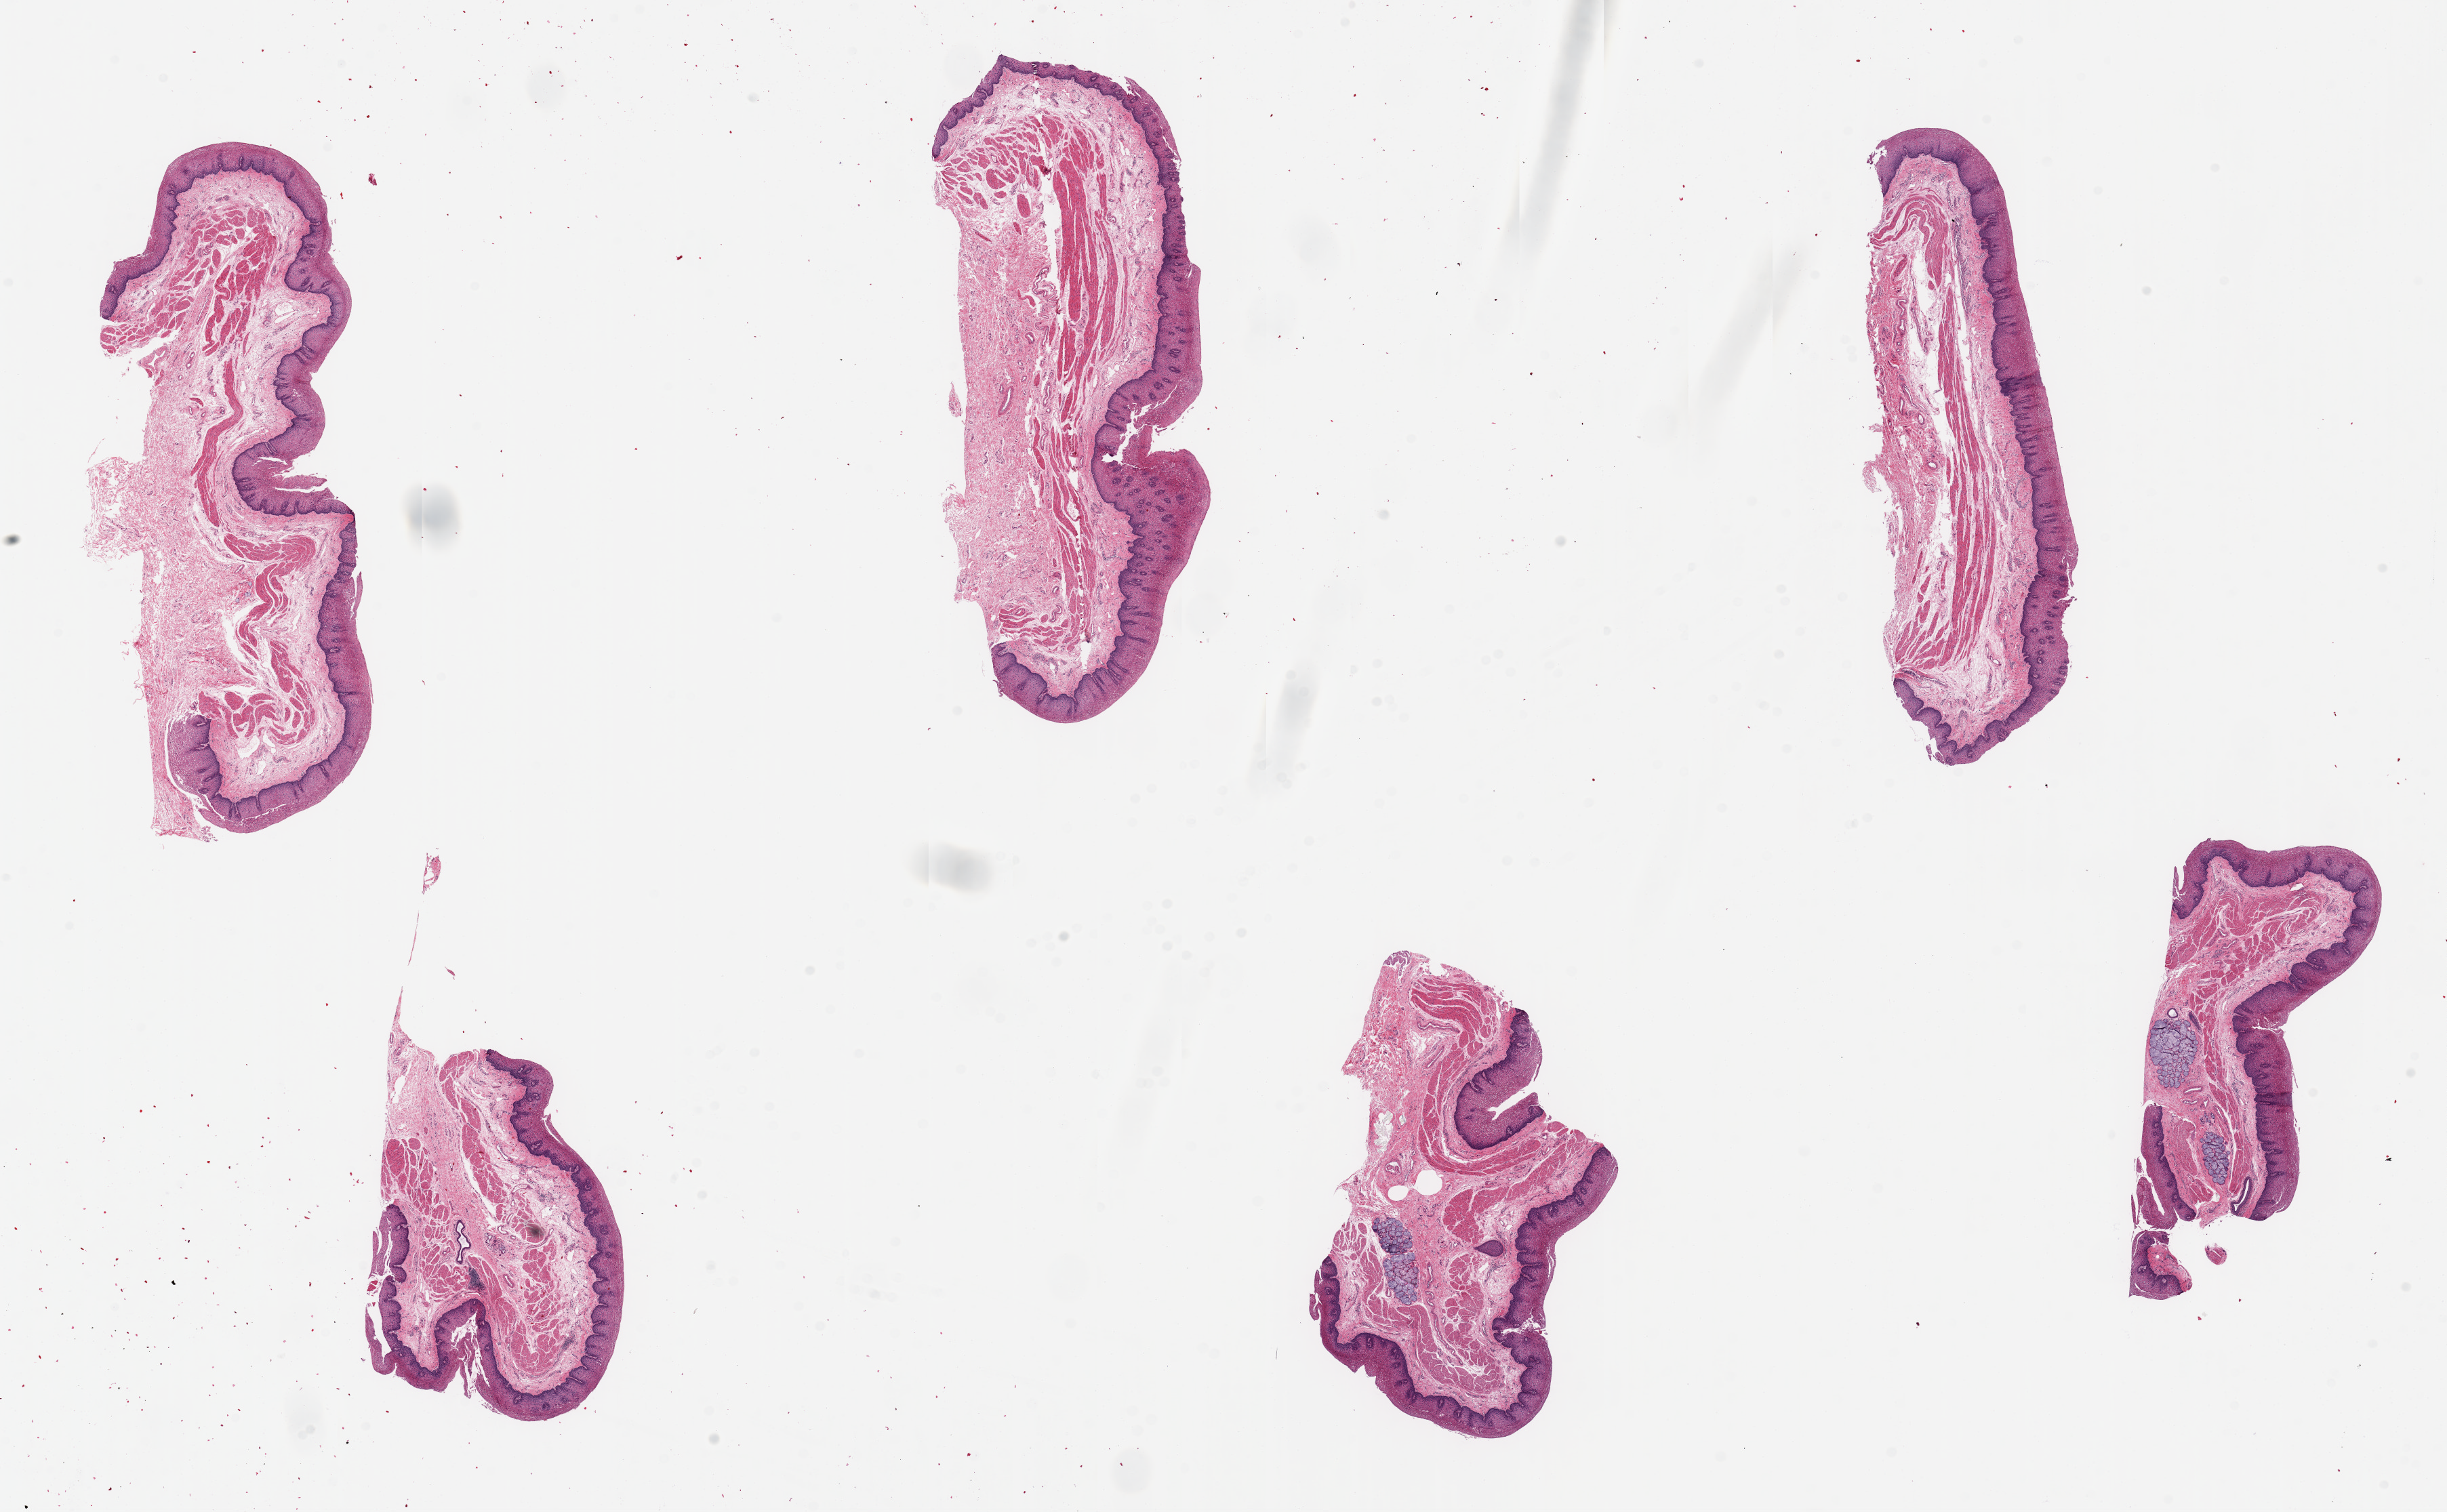
H&E whole-slide image, brightfield — shown as a low-resolution overview of the whole scanned area (about 28.5 x 17.6 mm), PAXgene-fixed paraffin-embedded (PFPE) section, target tissue: esophageal mucous membrane, donor tissue sample.
Pathologist's review note for this sample: 6 pieces, up to 8x3mm; squamous mucosa well preserved, up to ~10-25% thickness.